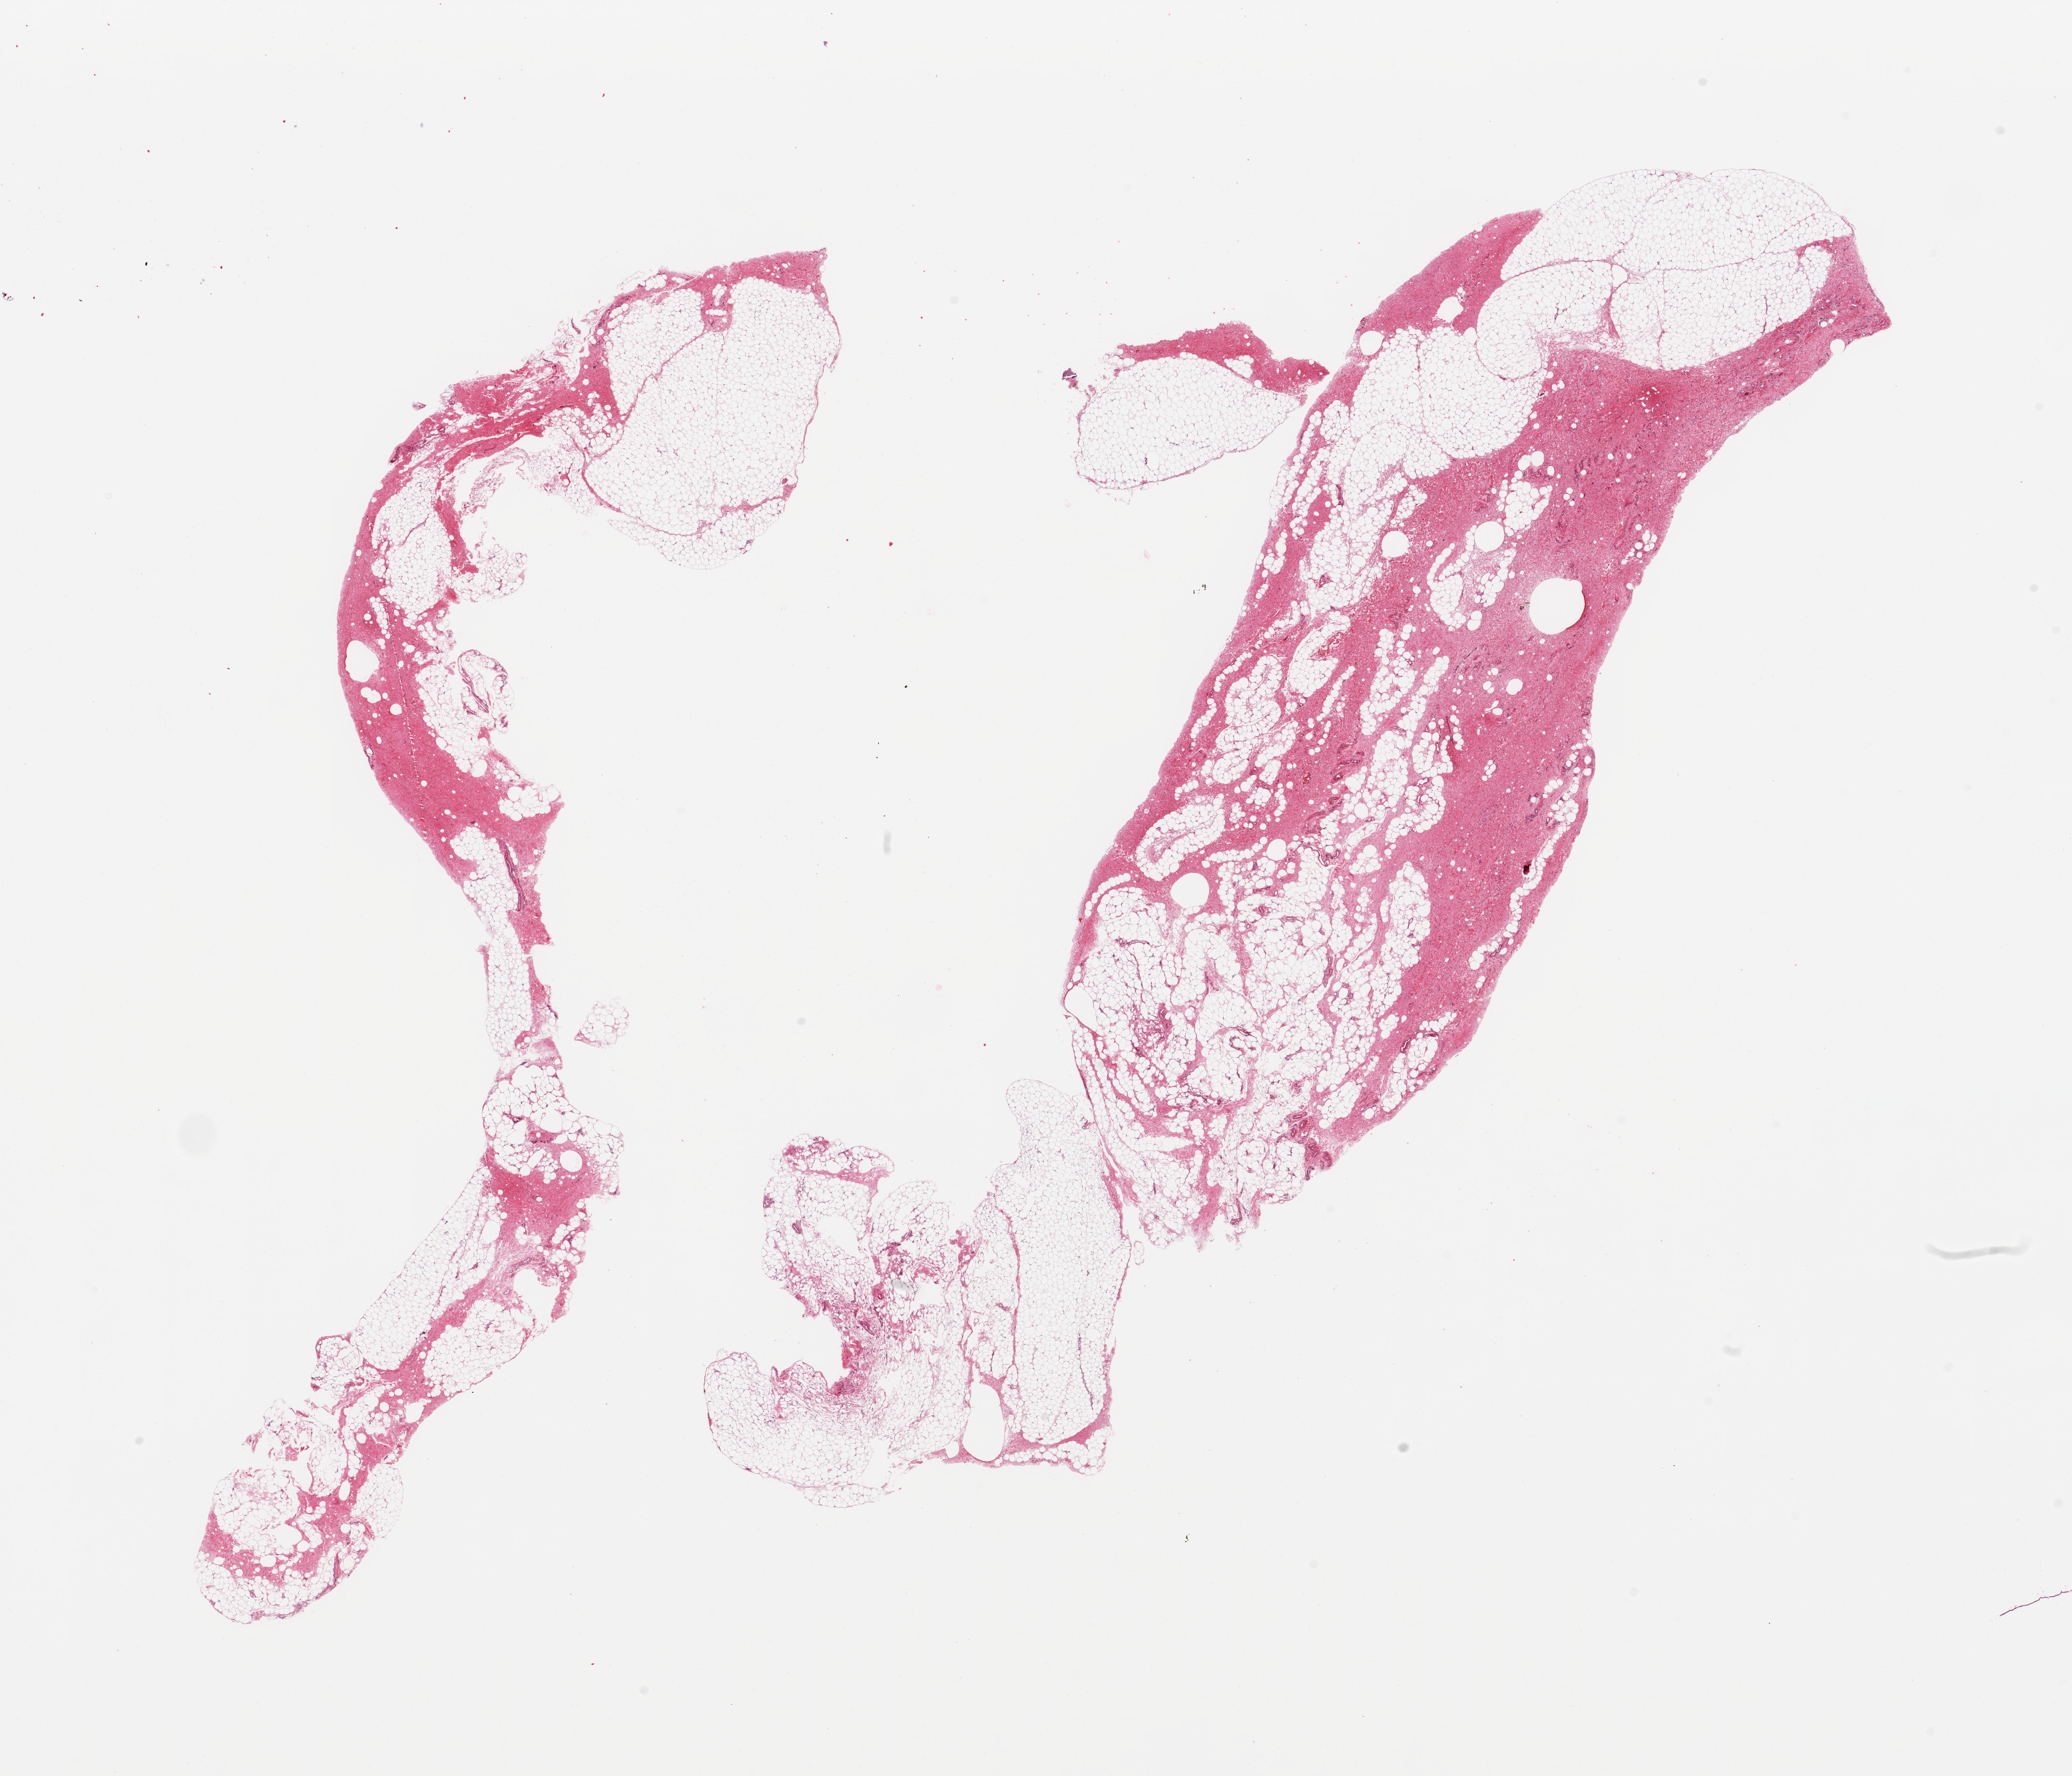
Haematoxylin and eosin whole-slide image, shown as a low-resolution overview of the whole scanned area (about 24.6 x 21.1 mm, from a 20x scan); PAXgene-fixed paraffin-embedded (PFPE) section; section of omentum (target tissue); donor tissue sample. Donor: female.
Review note (as recorded): 2 pieces; 50% fat/50% fibrous.